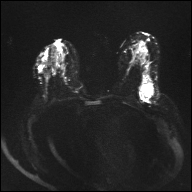
Breast MRI, one axial slice. Position 17 of 32 along the scan axis. Diffusion-weighted series; image 2 of 4 stored at this slice position (different b-values; order by instance number). 1.5 T. 192 × 192 image matrix, field of view 360 × 360 mm. Female patient.
Annotated regions visible in this slice (manually delineated by an expert):
- tumour on diffusion-weighted imaging: box from (x=140, y=83) to (x=151, y=97) px